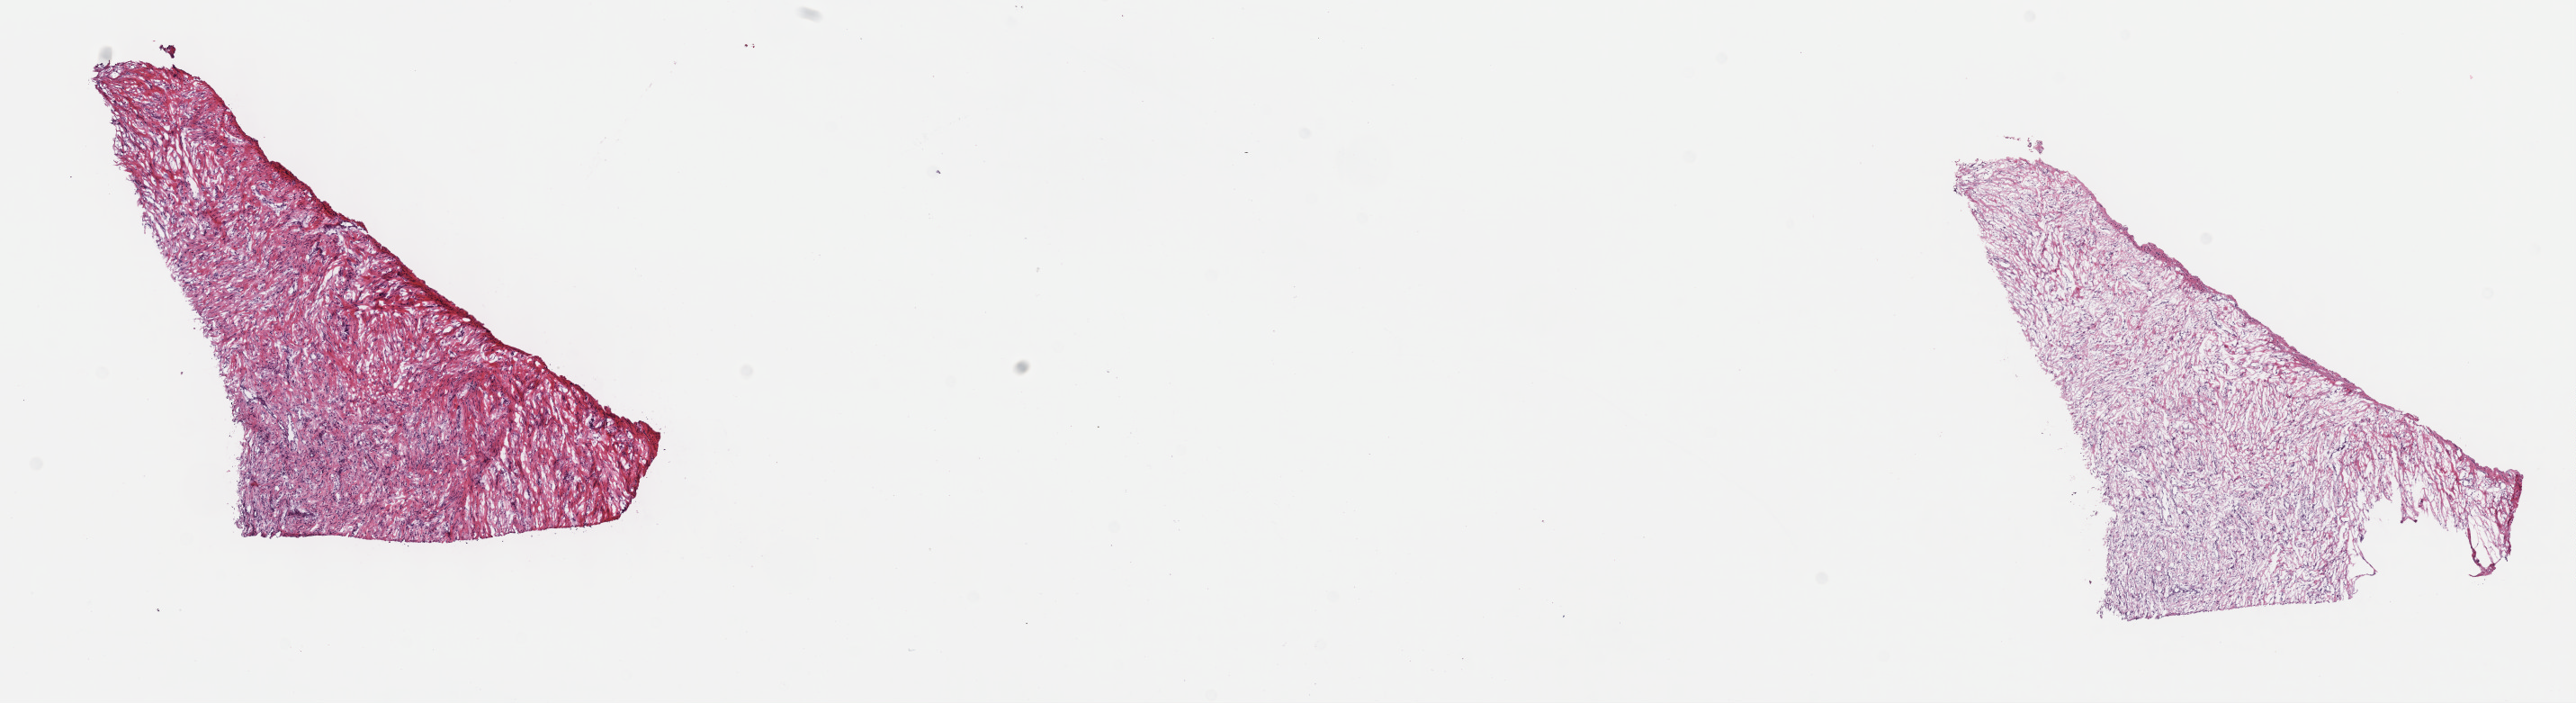
Hematoxylin and eosin (H&E) stained whole-slide image — a low-resolution overview of the entire scanned area, about 23.2 x 6.3 mm (from a 40x scan); frozen section from the top of the tissue portion; primary tumour sample from the connective, subcutaneous and other soft tissues. Patient: male, age at initial diagnosis 35 years. Pathologist review of this section (percent, as recorded): tumour cells 35%, tumour nuclei 100%, normal cells 0%, stromal cells 65%, necrosis 0%. Infiltration values recorded for this section: lymphocyte infiltration 0%, monocyte infiltration 0%, neutrophil infiltration 0%.
* pathologic diagnosis: Fibromyxosarcoma (connective, subcutaneous and other soft tissues of lower limb and hip)